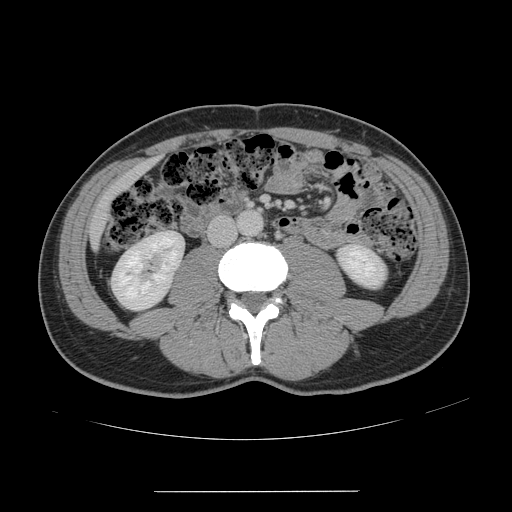
Contrast-enhanced abdominal CT, one axial slice; position 30 of 178 along the scan axis; intravenous contrast given; soft-tissue window (W 400 / L 40 HU); 2.5 mm slice thickness; 512 × 512 image matrix. Male patient, age 53 years. From the clinical record (not read from this slice): diagnosis: colorectal cancer liver metastases, imaged before liver resection; multiple liver metastases: yes; largest metastasis: 2.4 cm; disease in both lobes: no.
Structures marked on this image (expert manual segmentation):
- liver: box from (x=91, y=161) to (x=153, y=245) px